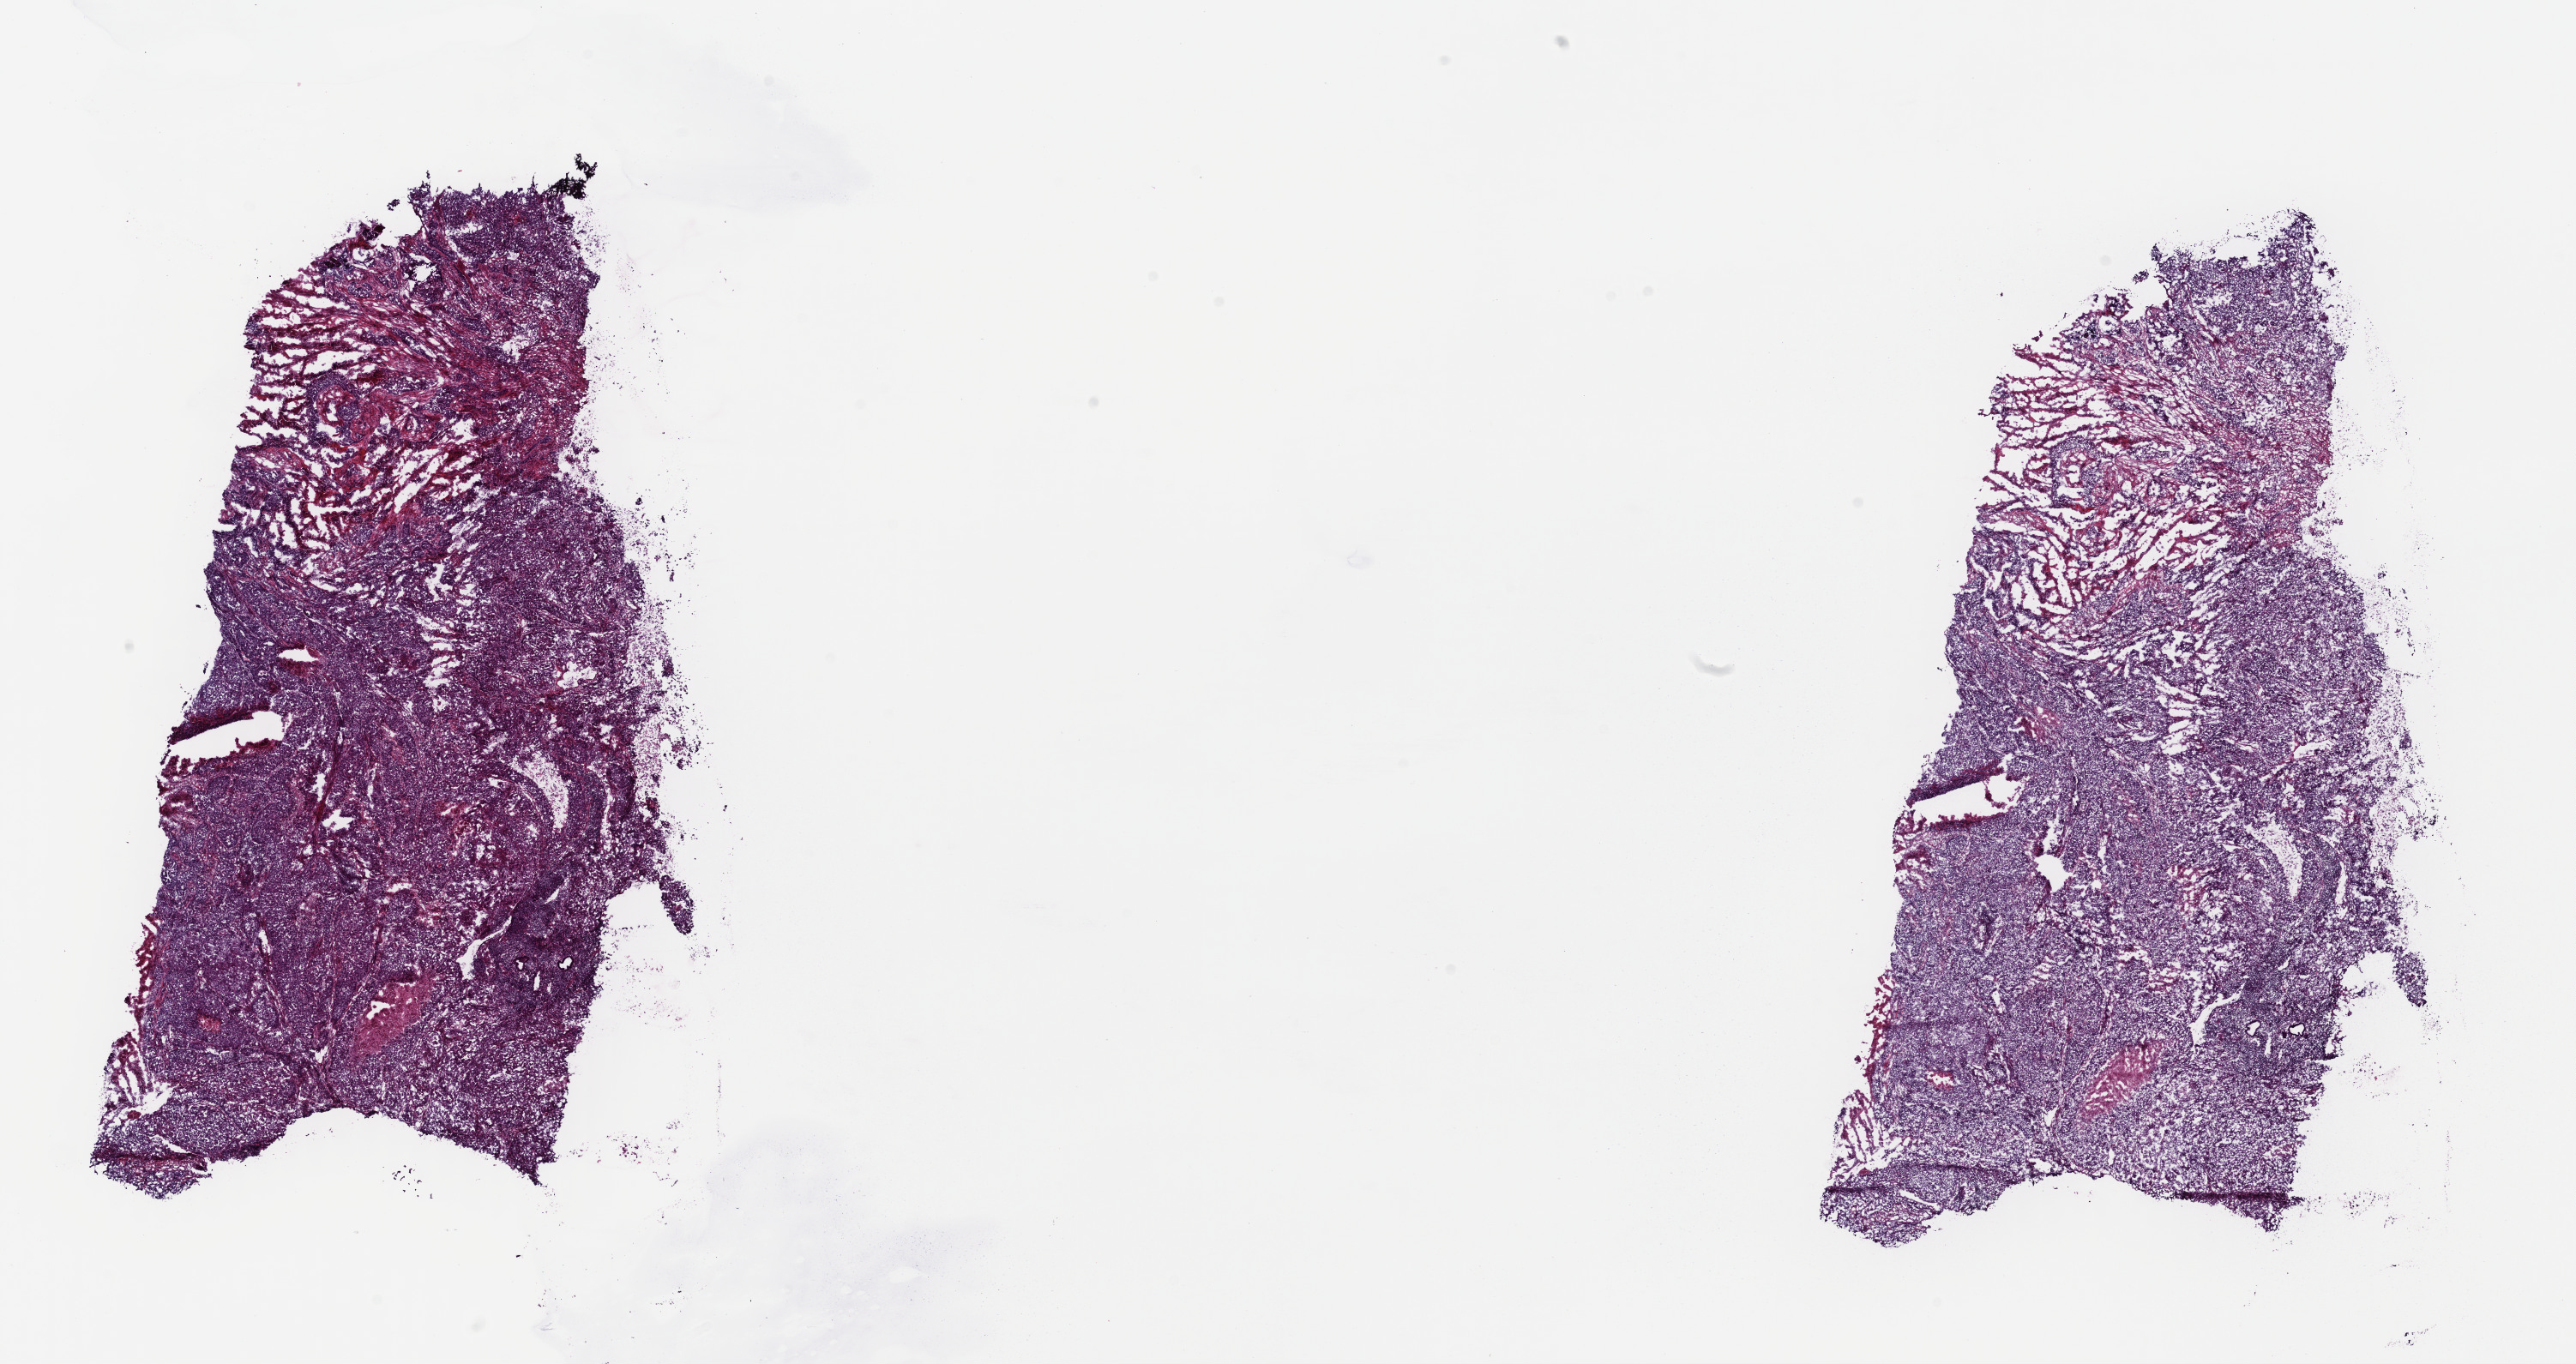
H&E whole-slide image, whole scanned area (about 23.7 x 12.6 mm) shown as a low-resolution overview; frozen section; uterus, primary tumour sample. Patient: female, age at initial diagnosis 84 years. Histologic grade: G3 (poorly differentiated). Pathologist review of this section (percent, as recorded): tumour cells 80%, tumour nuclei 80%, normal cells 0%, stromal cells 10%, necrosis 10%. Inflammatory infiltration, as recorded: lymphocyte infiltration 40%, monocyte infiltration 20%, neutrophil infiltration 20%.
• pathologic diagnosis: Endometrioid adenocarcinoma, NOS (endometrium)
• FIGO stage: IB